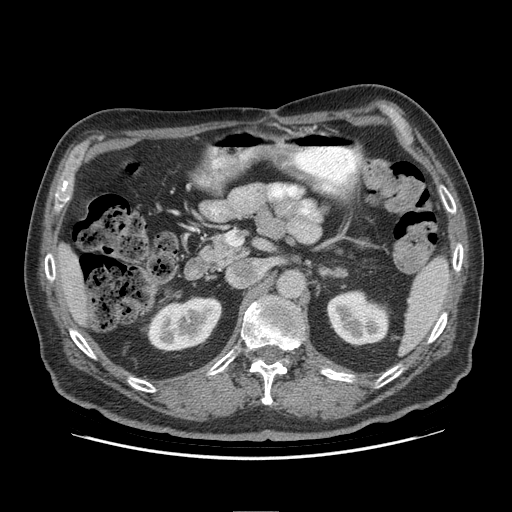
Contrast-enhanced abdominal CT (liver protocol), one axial slice. Position 47 of 95 along the scan axis. 140 kVp. Soft-tissue window (W 400 / L 40 HU). 2.5 mm slice thickness. 512 × 512 image matrix, field of view 400 × 400 mm. Case-level facts recorded for this patient, not image findings: diagnosis: hepatocellular carcinoma (patient treated with transarterial chemoembolisation; whether this scan precedes or follows treatment is not stated here); TNM stage (as recorded): Stage-IVB; Child-Pugh class: A; tumour differentiation: well differentiated.
Outlined on this slice (semi-automatic segmentation, software-assisted and operator-edited):
- liver parenchyma outside the tumour (the mass and vessels are separate outlines, so this box may not span the whole liver): bounding box (x1, y1, x2, y2) in pixels: (56, 243, 92, 326)